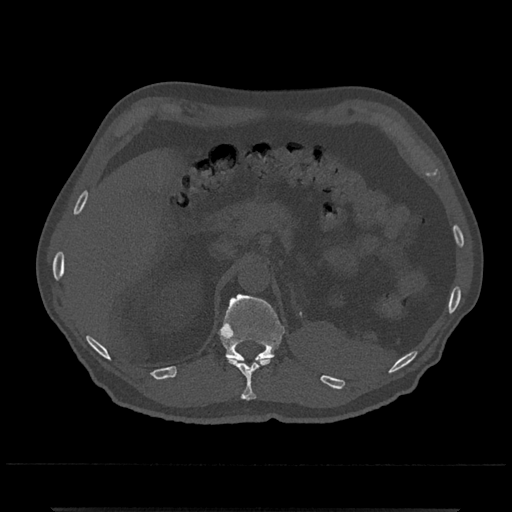
CT including the spine, one axial slice. Position 454 of 797 along the scan axis. 120 kVp. Bone window (W 1800 / L 400 HU). 512 × 512 image matrix. Male patient, age 67 years. From the clinical record (not read from this slice): primary cancer: prostate.
Annotated regions visible in this slice (semi-automatic segmentation, software-assisted and operator-edited):
- T11 vertebra: box from (x=228, y=356) to (x=274, y=400) px
- T12 vertebra: (x=218, y=294)–(x=285, y=363)